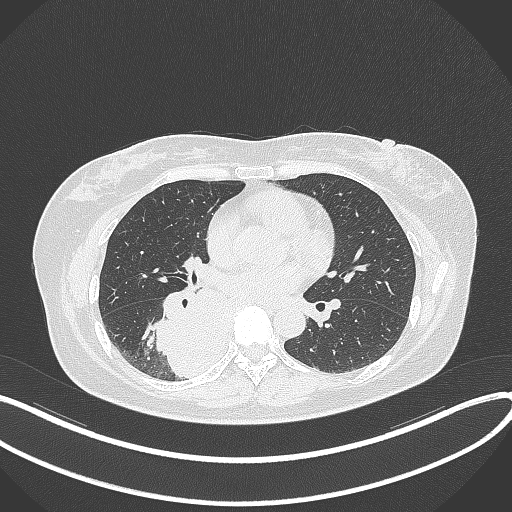
Chest CT, one axial slice; slice 174 of 331 in the series (ordered by position); reconstruction kernel B70f; lung window (W 1500 / L -600 HU); 512 × 512 image matrix, field of view 400 × 400 mm. Patient: female, 54 years. Case-level facts recorded for this patient, not image findings: clinical TNM (as recorded): T4 N0 M0.
Structures marked on this image (bounding box drawn by a radiologist):
- lung tumour (recorded histology: adenocarcinoma): bounding box [x1, y1, x2, y2] px = [147, 282, 239, 378]